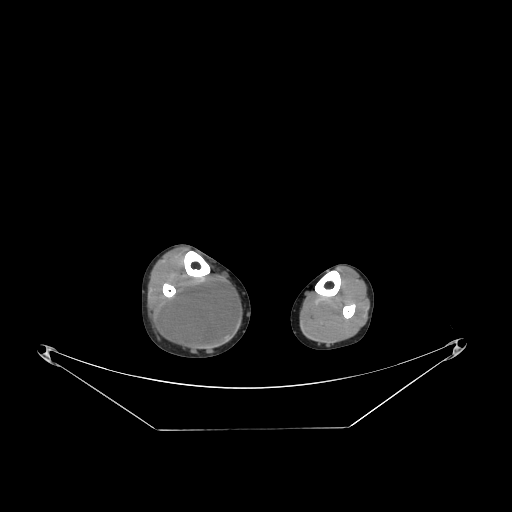
CT of an extremity soft-tissue mass (from a PET/CT study), one axial slice; slice 83 of 267 in the series (ordered by position); reconstruction kernel STANDARD; 140 kVp; soft-tissue window (W 400 / L 40 HU); 3.75 mm slice thickness; 512 × 512 image matrix, field of view 500 × 500 mm. Male patient. From the clinical record (not read from this slice): histological type: liposarcoma - round cell; grade: high; site of the primary tumour: right calf.
Annotated regions visible in this slice (expert contour drawn on MRI and transferred to this co-registered scan by the dataset authors):
- gross tumour volume (mass): bounding box (x1, y1, x2, y2) in pixels: (162, 276, 239, 346)